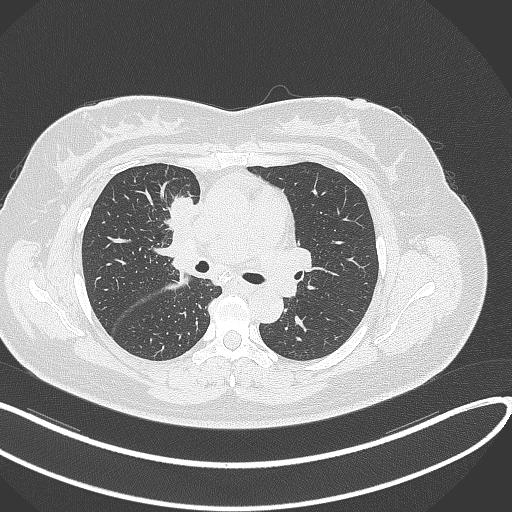
Chest CT, one axial slice. Position 165 of 303 along the scan axis. Reconstruction kernel B70f. 120 kVp. Lung window (W 1500 / L -600 HU). 1 mm slice thickness. 512 × 512 image matrix. Female patient, age 46 years. Case-level facts recorded for this patient, not image findings: clinical TNM (as recorded): T2a N1 M0.
Outlined on this slice (rectangle marked by the reading radiologist):
- lung tumour (recorded histology: adenocarcinoma): bounding box (x1, y1, x2, y2) in pixels: (165, 193, 201, 232)